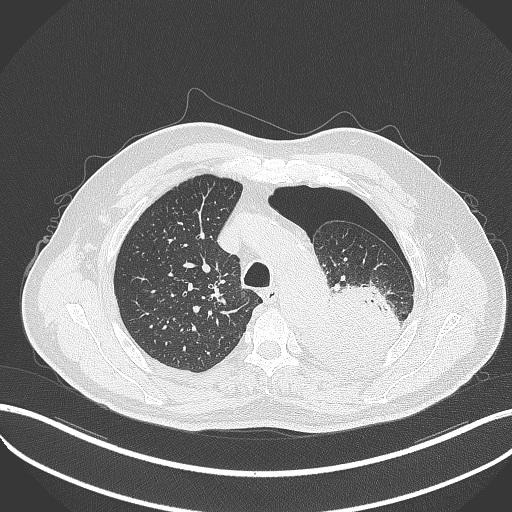
Chest CT, one axial slice. Position 385 of 464 along the scan axis. Reconstruction kernel B70f. 120 kVp. Lung window (W 1500 / L -600 HU). 1 mm slice thickness. 512 × 512 image matrix. Patient: male, 76 years. From the clinical record (not read from this slice): clinical TNM (as recorded): T3 N0 M1b.
Outlined on this slice (bounding box drawn by a radiologist):
- lung tumour (recorded histology: adenocarcinoma): box from (x=299, y=284) to (x=406, y=378) px